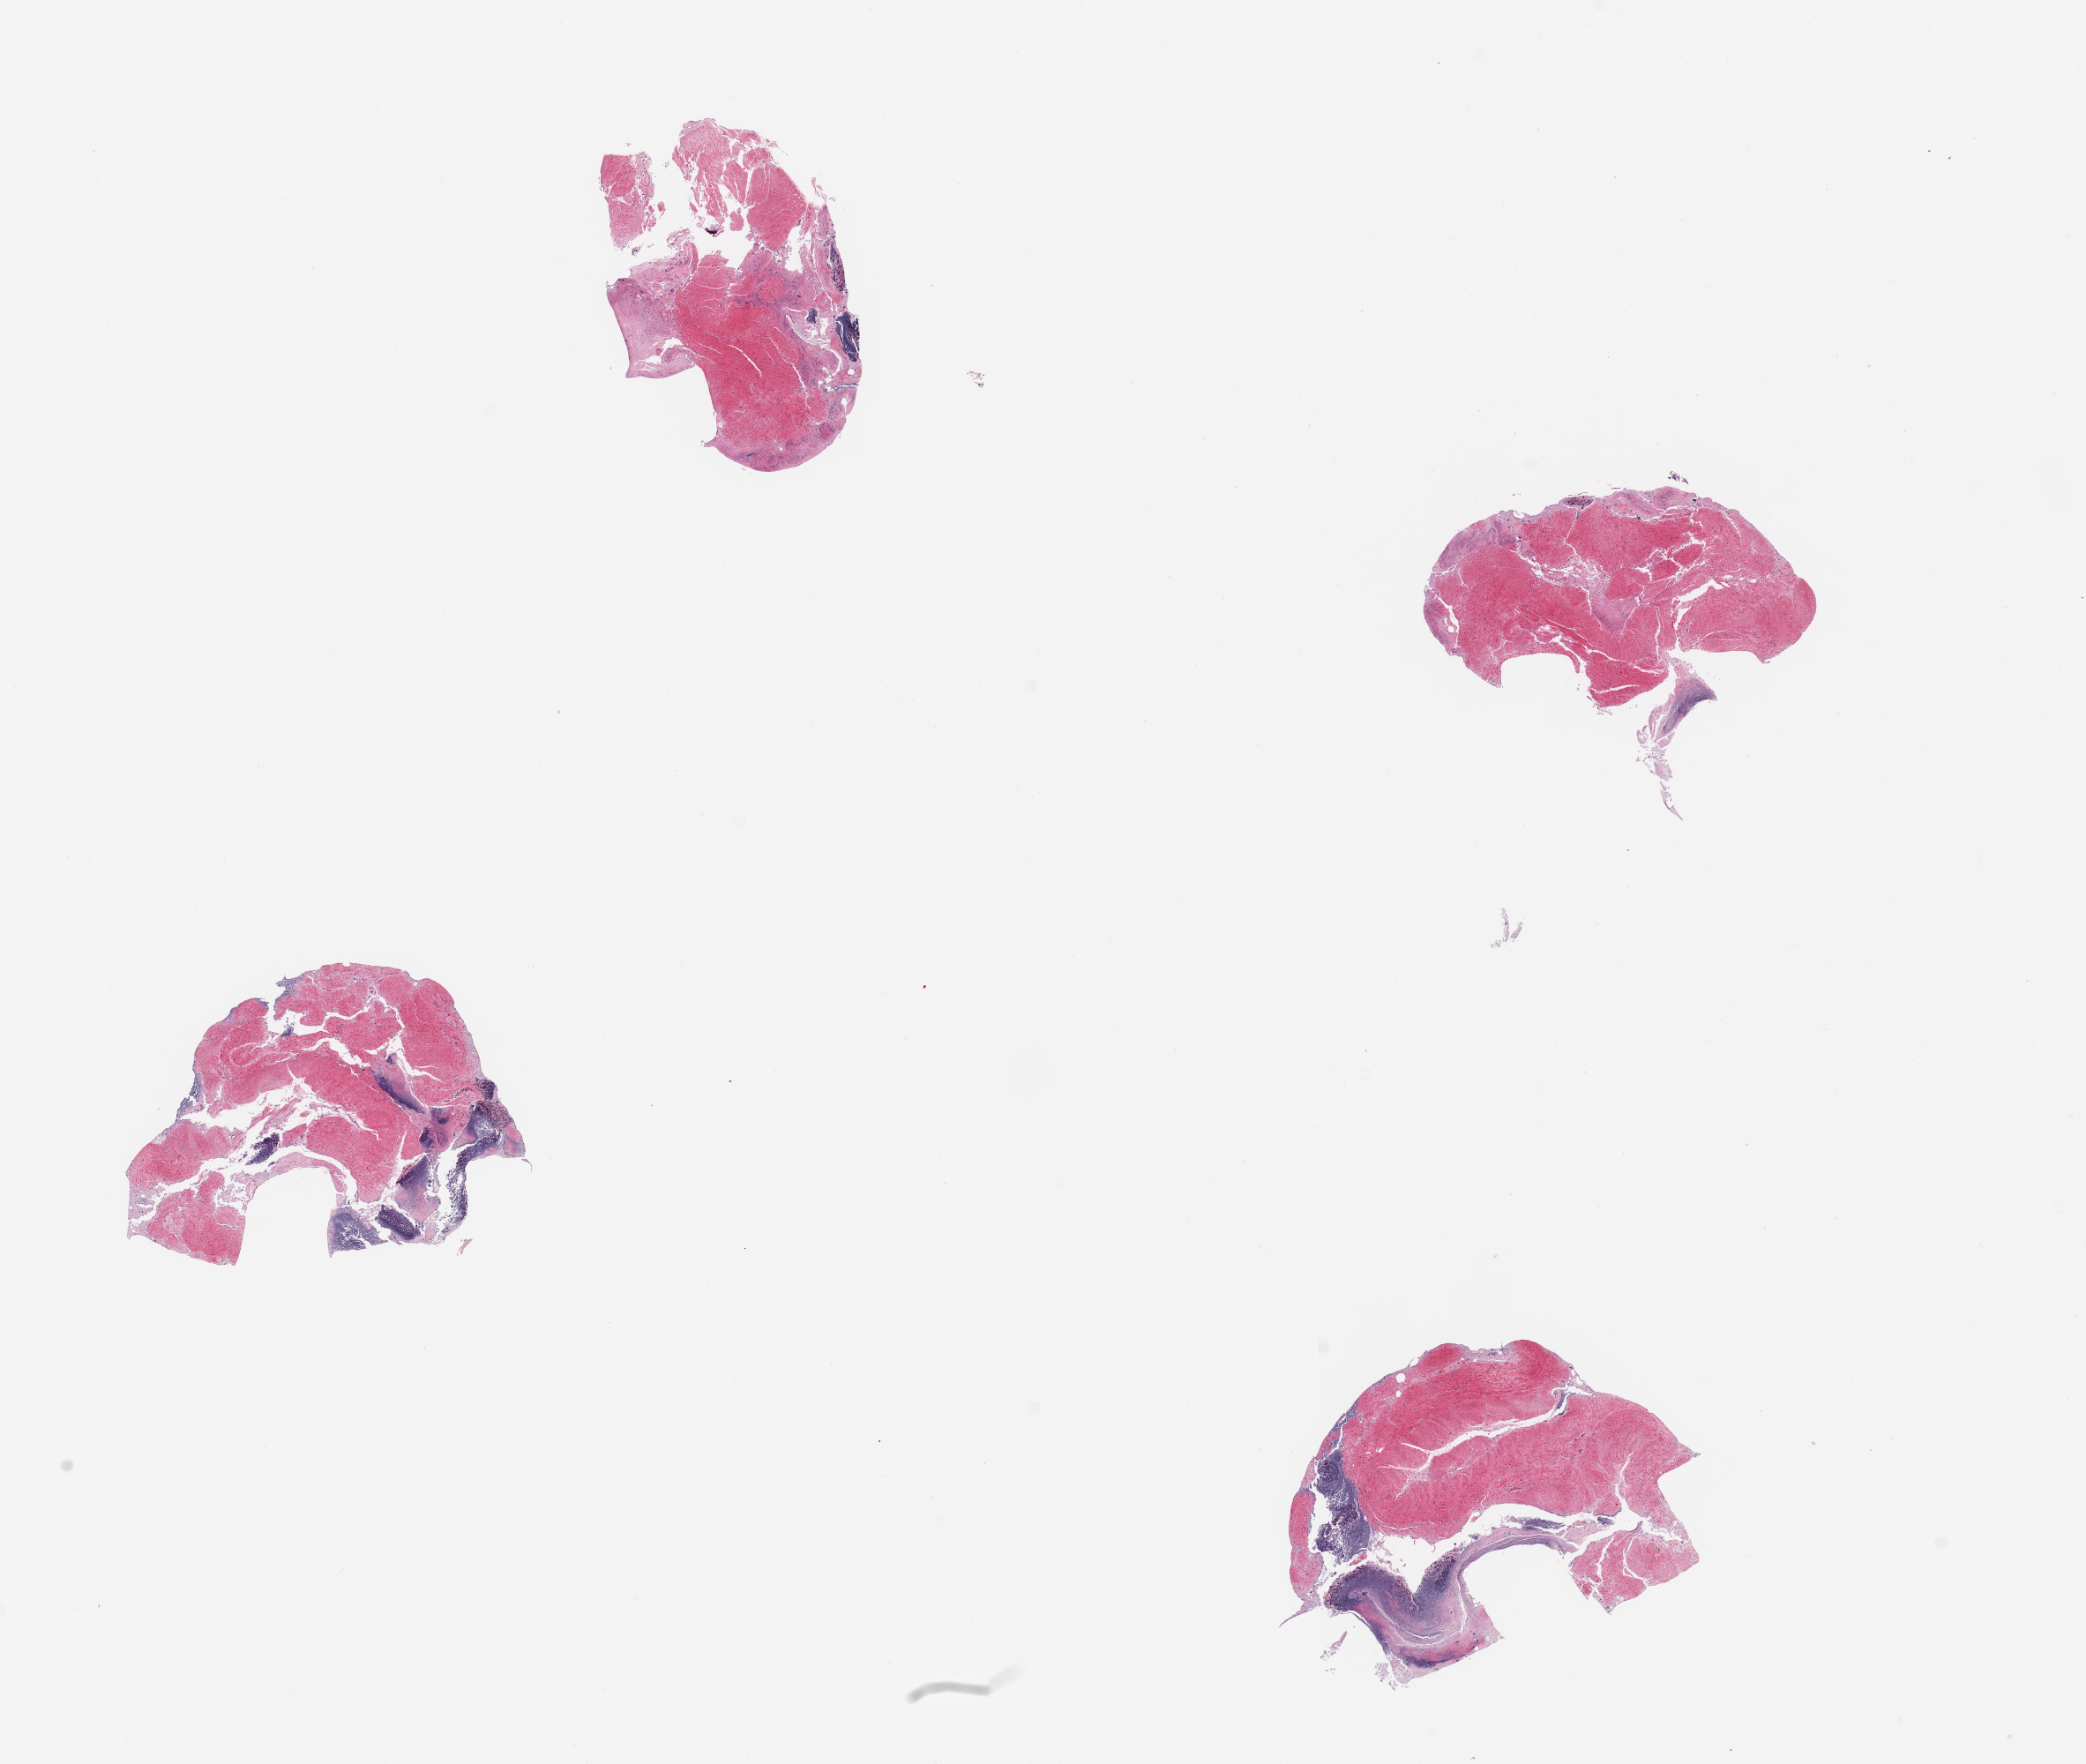
Digitized hematoxylin and eosin (H&E)-stained section — a low-resolution overview of the entire scanned area, about 18.7 x 15.8 mm (slide scanned at 20x); PAXgene-fixed, paraffin-embedded tissue; target tissue: ileum; tissue donor sample. Male donor.
Reviewer comment on this tissue sample: 4 pieces; good lymphoid component, but very autolyzed, muscularis (not target) also present.